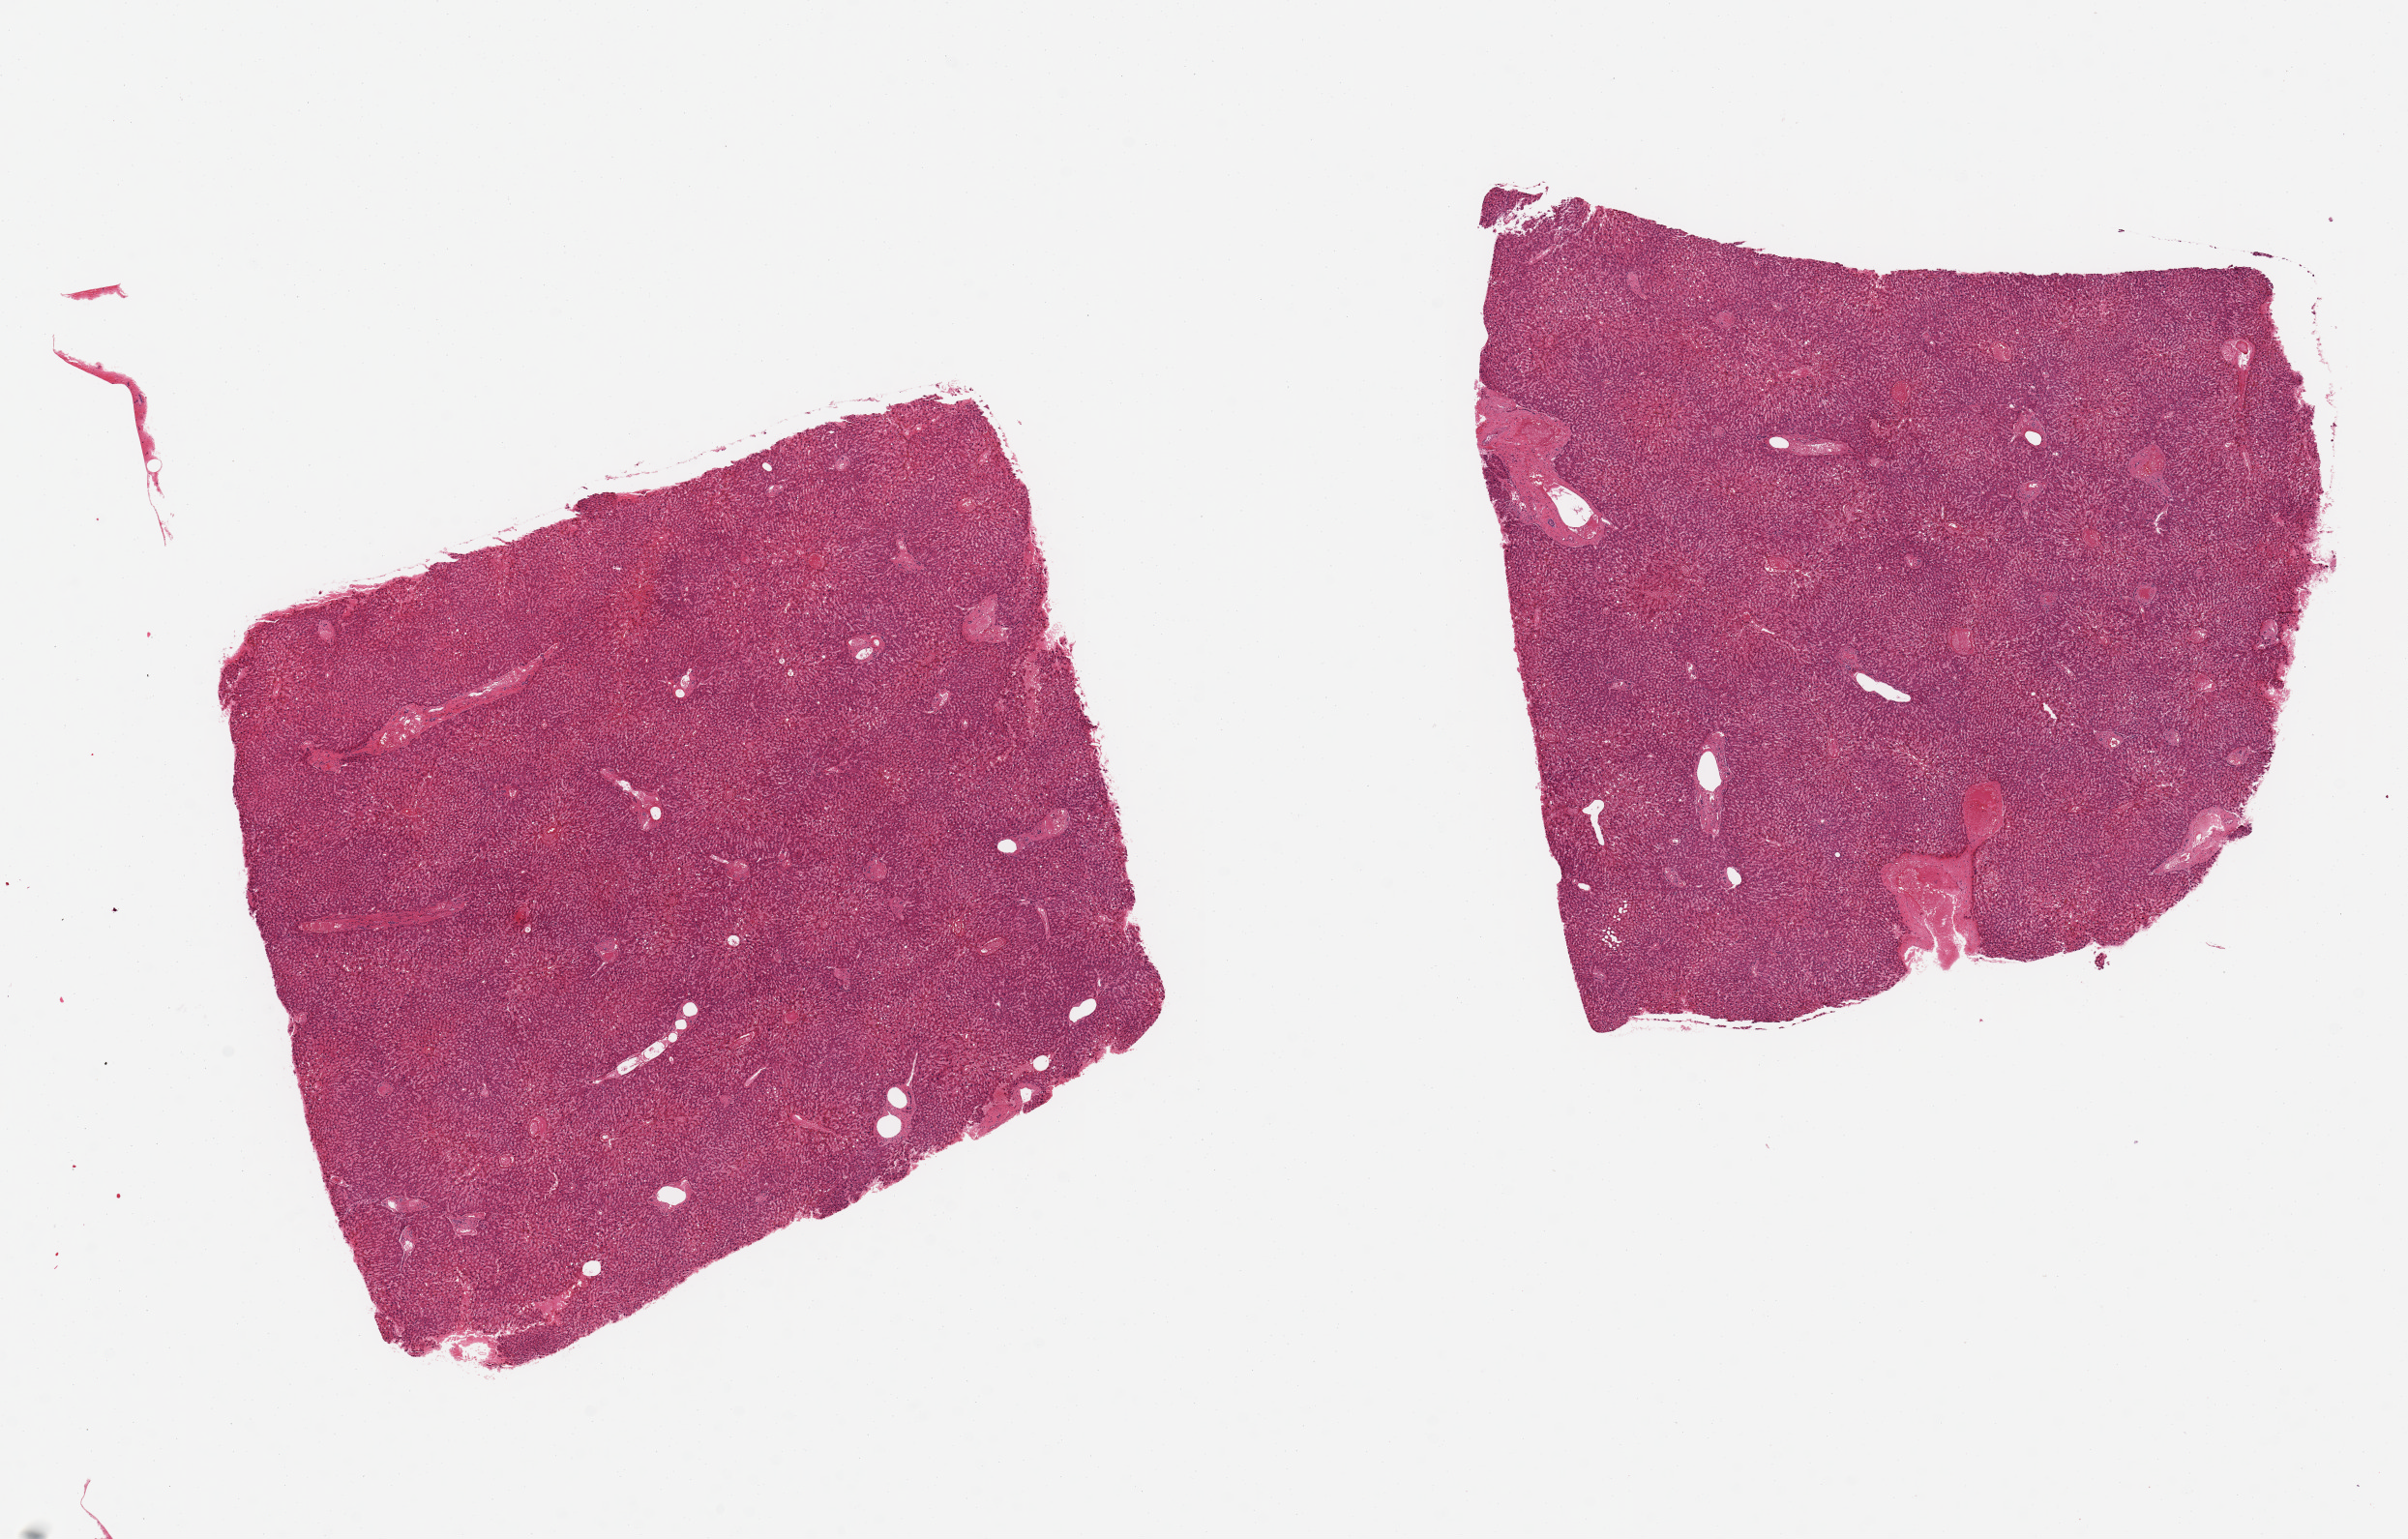
Whole-slide image, H&E stain, brightfield, whole scanned area (about 19.7 x 12.6 mm) shown as a low-resolution overview; PAXgene-fixed, paraffin-embedded tissue; sampled site (target tissue): liver; tissue donor sample. Donor: female.
Pathologist's review note for this sample: 2 pieces, 7x6 & 7x6 mm; no lesions.